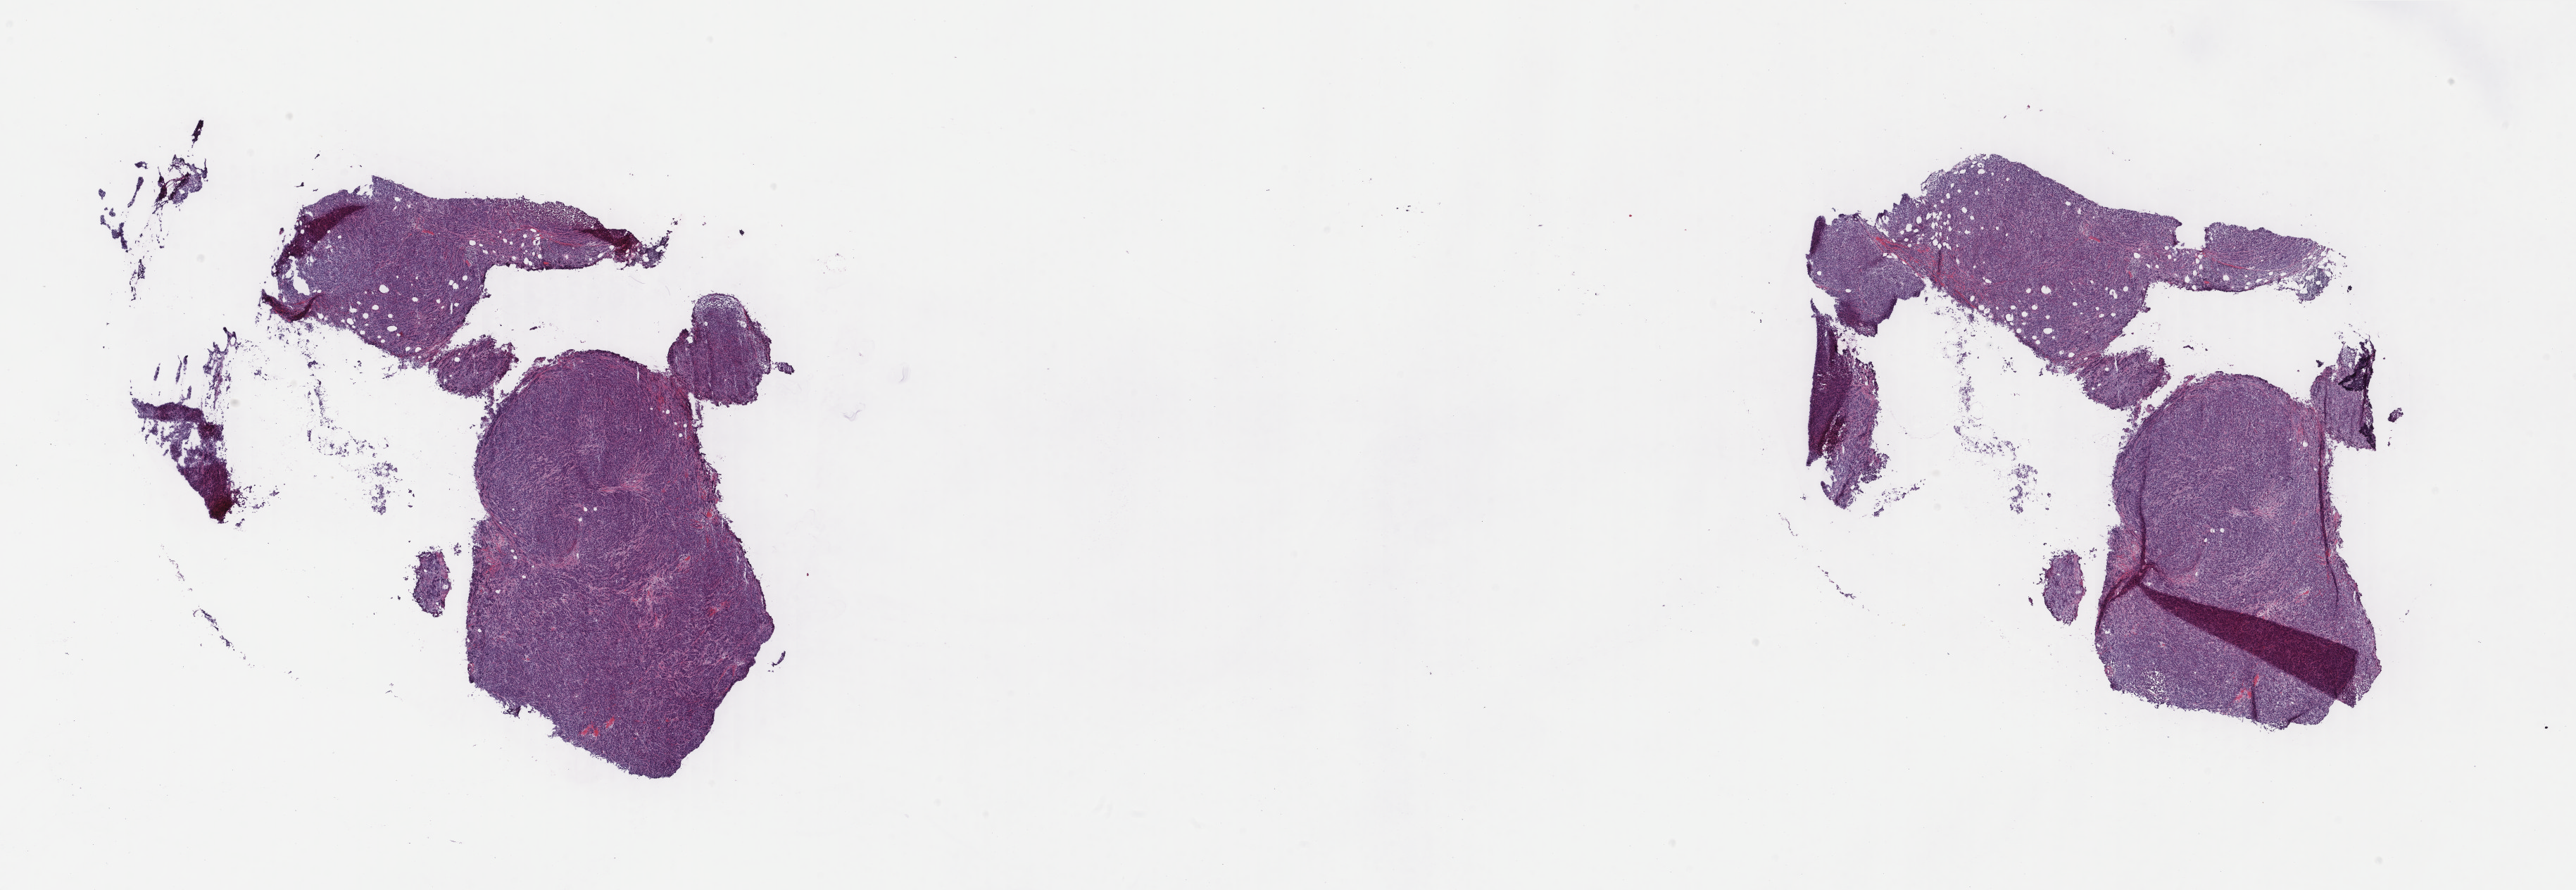
H&E-stained whole-slide image — a low-resolution overview of the entire scanned area, about 29.0 x 10.0 mm (from a 40x scan); frozen section from the top of the tissue portion; primary tumour sample from the breast. Female, age 61 years at initial diagnosis. Pathologist review of this section (percent, as recorded): tumour cells 93%, tumour nuclei 93%, normal cells 0%, stromal cells 6%, necrosis 1%. Inflammatory infiltration, as recorded: lymphocyte infiltration 5%, monocyte infiltration 0%, neutrophil infiltration 0%.
Pathologic diagnosis: Infiltrating duct carcinoma, NOS. Lymph nodes positive (case pathology): 0 of 15 examined. AJCC pathologic stage: IIA.